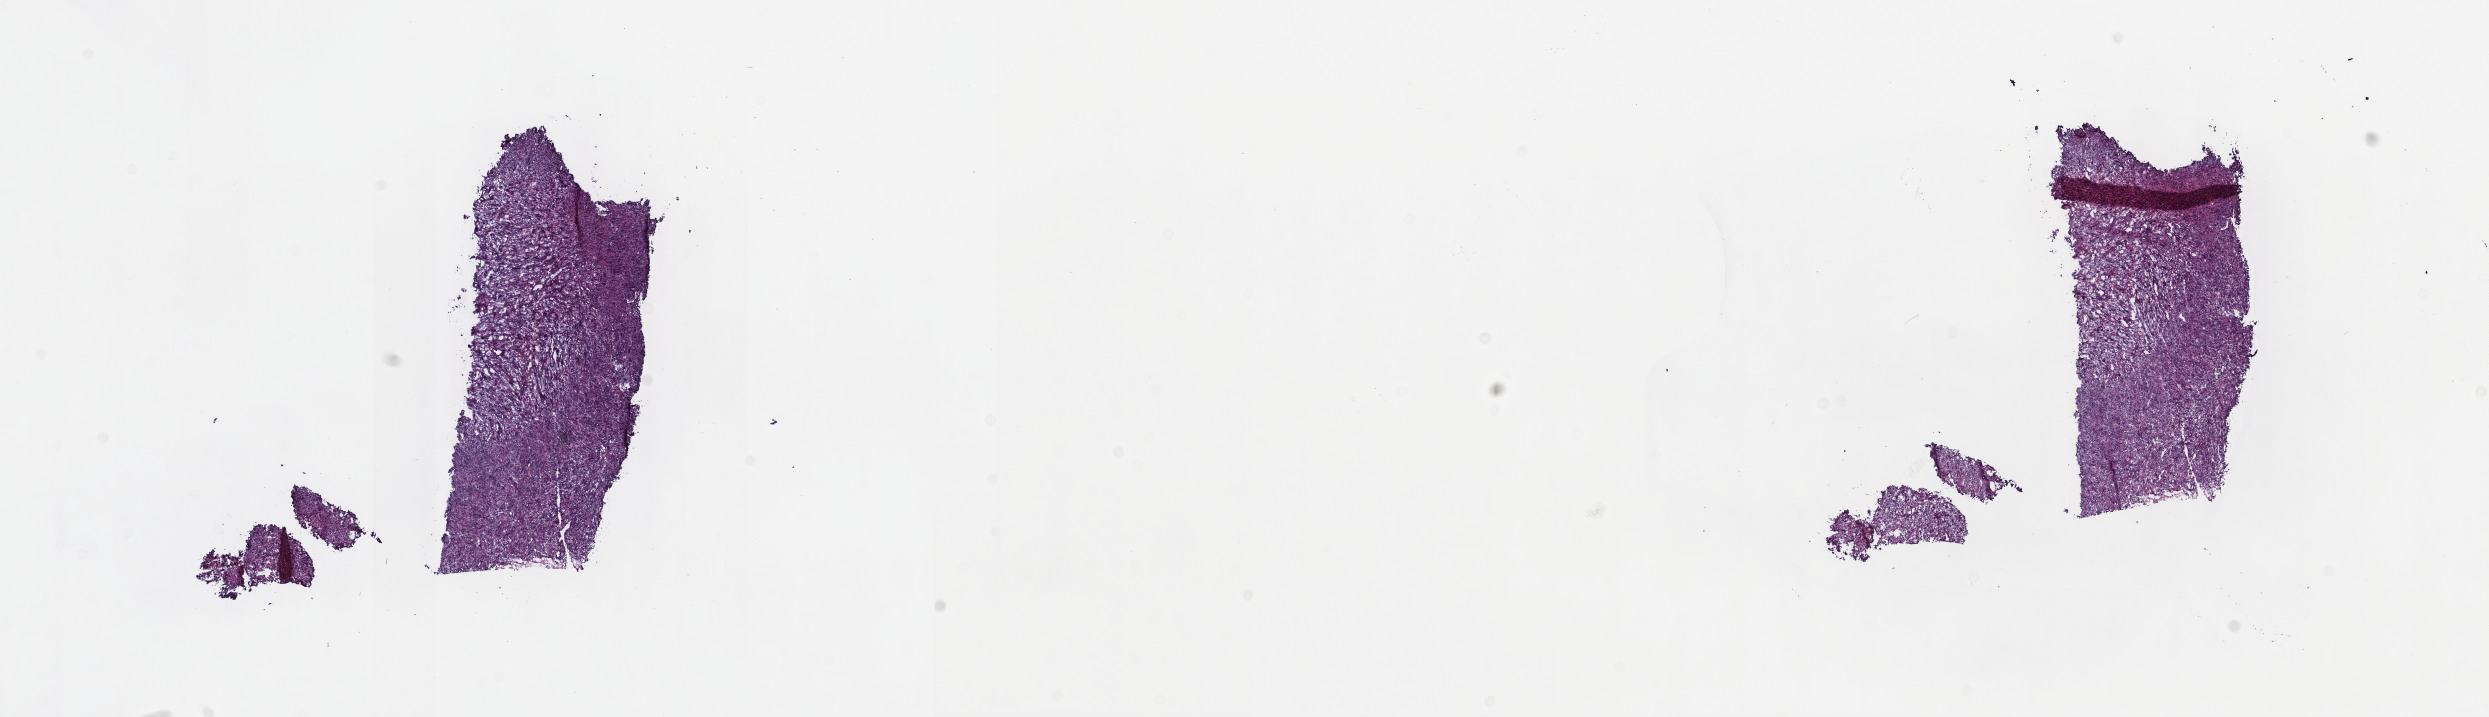
H&E whole-slide image, whole scanned area (about 20.1 x 5.8 mm, from a 40x scan) shown as a low-resolution overview. Frozen section. Sample: primary tumour, retroperitoneum and peritoneum. Male, age 70 years at initial diagnosis. Composition of this section per pathologist review: tumour cells 100%, tumour nuclei 80%, normal cells 0%, stromal cells 0%, necrosis 0%. Inflammatory infiltration, as recorded: lymphocyte infiltration 1%, monocyte infiltration 0%, neutrophil infiltration 0%.
- pathologic diagnosis: Leiomyosarcoma, NOS (retroperitoneum)